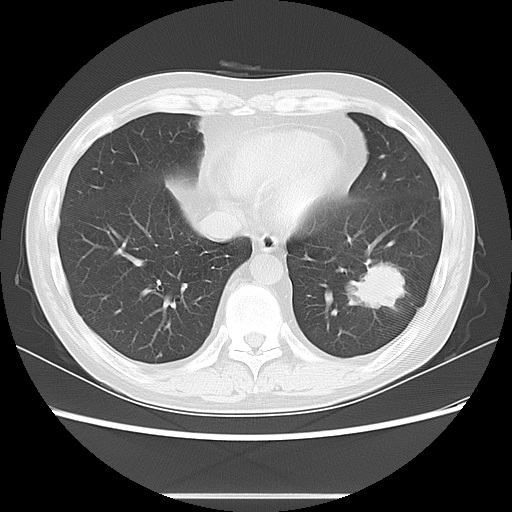
Chest CT, one axial slice. Position 24 of 63 along the scan axis. 120 kVp. Lung window (W 1500 / L -600 HU). 5 mm slice thickness. 512 × 512 image matrix, field of view 347 × 347 mm. Male patient, age 49 years. From the clinical record (not read from this slice): clinical TNM (as recorded): T3 N0 M0; histopathological grade: G2-3.
Structures marked on this image (rectangle marked by the reading radiologist):
- lung tumour (recorded histology: squamous cell carcinoma): bounding box (x1, y1, x2, y2) in pixels: (339, 256, 417, 322)